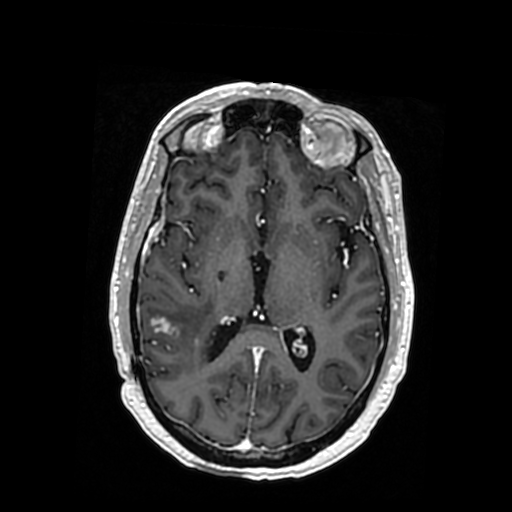
Brain MRI from a brain-tumour surgery series, one axial slice; slice 181 of 364 in the series (ordered by position); T1-weighted post-contrast; 0.5 mm slice thickness; 512 × 512 image matrix, field of view 260 × 260 mm. From the clinical record (not read from this slice): histopathology: Oligodendroglioma; WHO grade: 3; IDH mutation: yes; tumour location: Right Posterior Temporal Inferior Parietal.
Outlined on this slice (outlined manually by an expert reader):
- tumour: bounding box (x1, y1, x2, y2) in pixels: (146, 315, 217, 342)